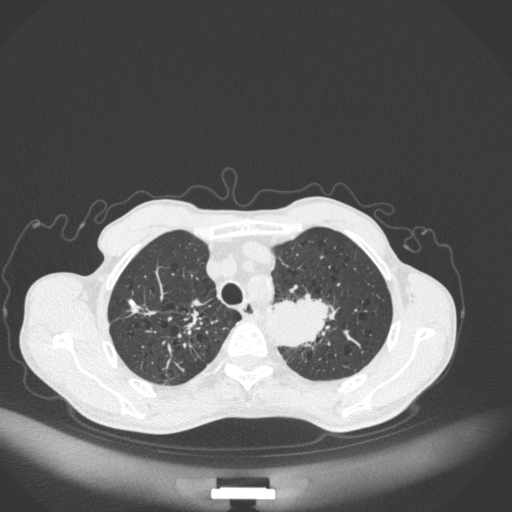
Chest CT, one axial slice; position 345 of 394 along the scan axis; reconstruction kernel B31f; 120 kVp; lung window (W 1500 / L -600 HU); 1 mm slice thickness; 512 × 512 image matrix, field of view 400 × 400 mm. Male patient, age 65 years. From the clinical record (not read from this slice): clinical TNM (as recorded): T2b N0 M0; histopathological grade: G2.
Structures marked on this image (bounding box drawn by a radiologist):
- lung tumour (recorded histology: adenocarcinoma): box from (x=269, y=293) to (x=331, y=350) px